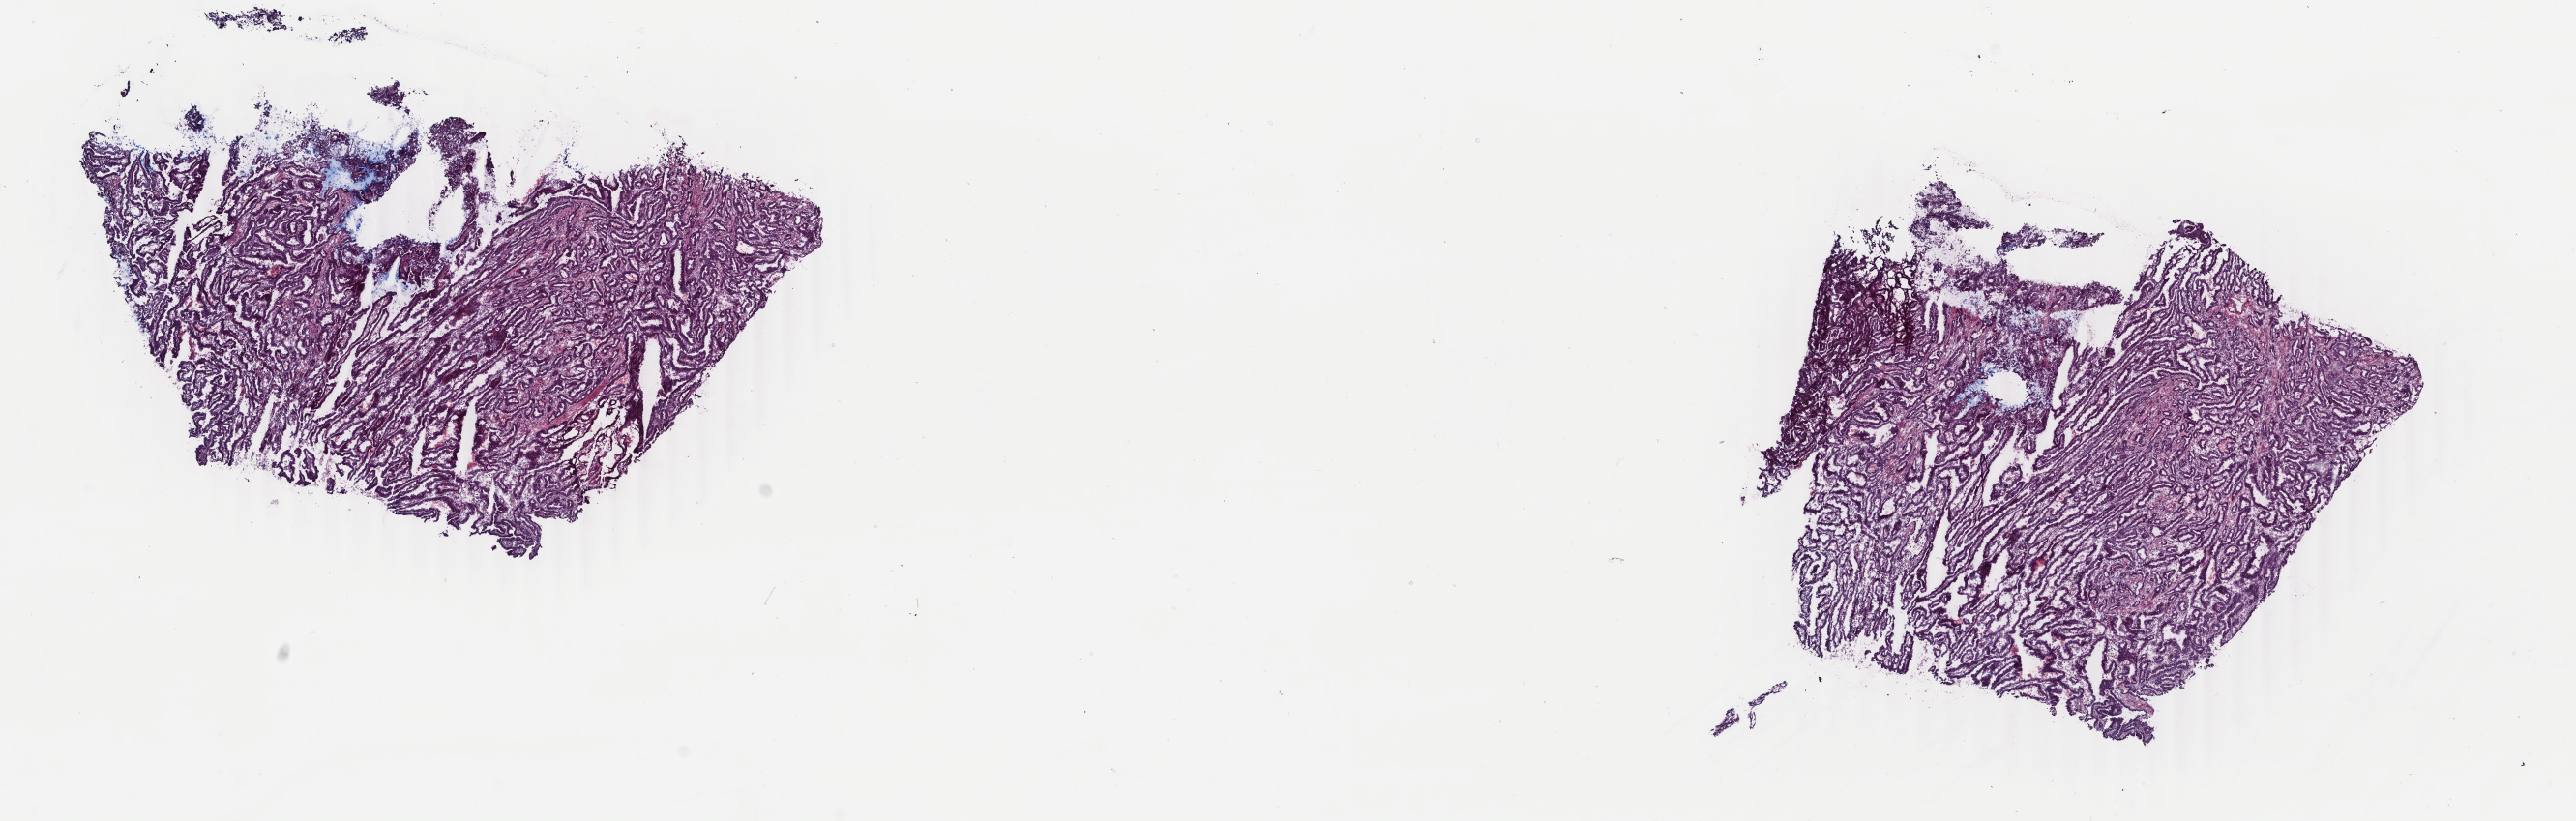
Whole-slide histology image, Hematoxylin and eosin (H&E) stained, a low-resolution overview of the entire scanned area, about 21.2 x 6.8 mm (acquisition: 40x scan); frozen section; primary tumour sample from the stomach. Male patient; age at initial diagnosis 56 years. Histologic grade: G2 (moderately differentiated). Slide review estimates, as recorded: tumour cells 60%, tumour nuclei 80%, normal cells 0%, stromal cells 32%, necrosis 8%. Infiltration values recorded for this section: lymphocyte infiltration 3%, monocyte infiltration 1%, neutrophil infiltration 0%.
Histologic diagnosis: Tubular adenocarcinoma (cardia, NOS). AJCC pathologic stage: IIIA (7th edition). Lymph nodes positive (case pathology): 14 of 14 examined.